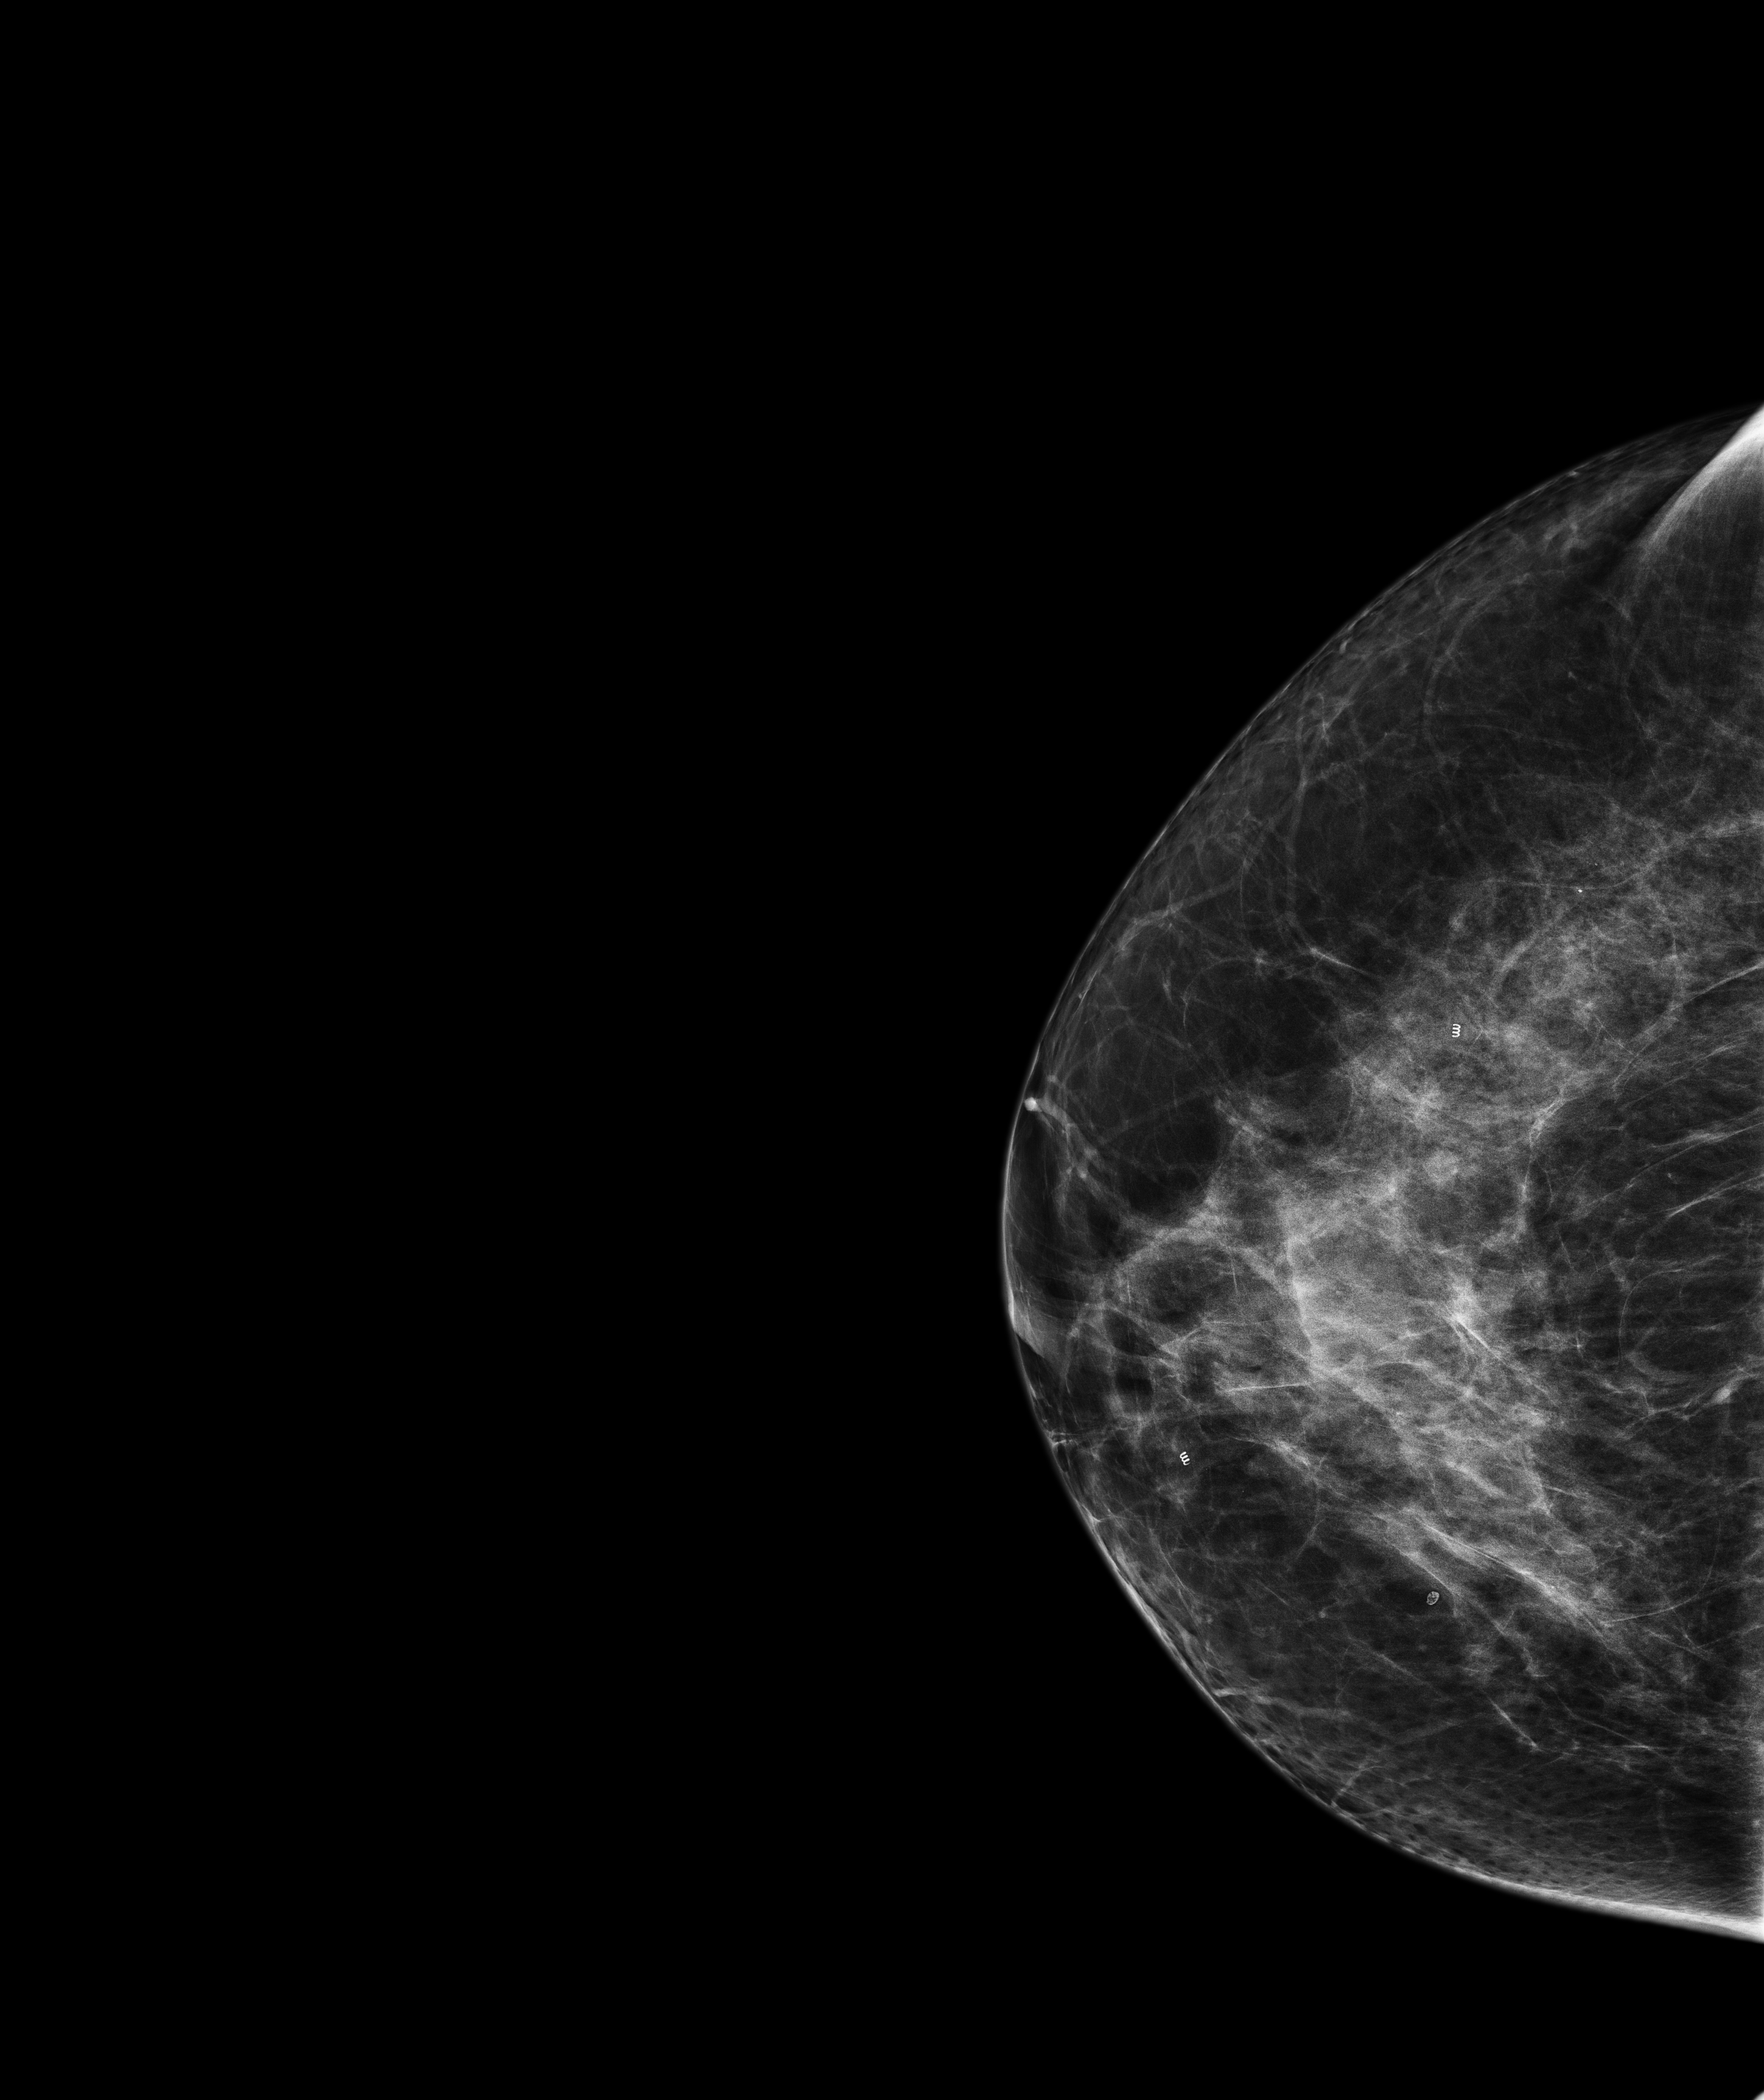
Screening examination; system: Senographe Pristina. Patient aged 48 years (female).
Image type: full-field digital mammogram. Breast: right. Projection: craniocaudal (CC) view.